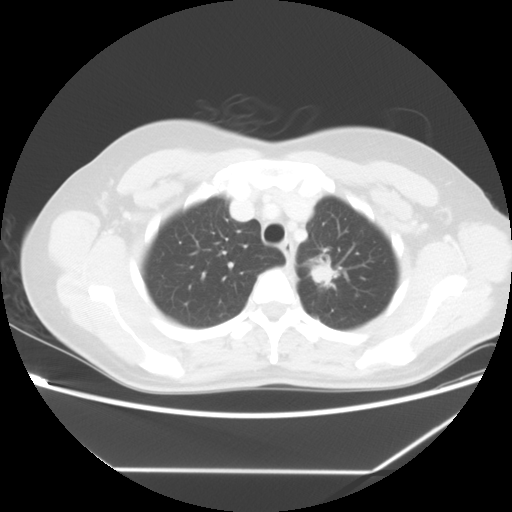
Chest CT, one axial slice. Slice 48 of 60 in the series (ordered by position). Reconstruction kernel STANDARD. 140 kVp. Lung window (W 1500 / L -600 HU). 512 × 512 image matrix, field of view 367 × 367 mm. Female patient, age 43 years. Case-level facts recorded for this patient, not image findings: clinical TNM (as recorded): T1c N0 M1b.
Annotated regions visible in this slice (bounding box drawn by a radiologist):
- lung tumour (recorded histology: adenocarcinoma): box from (x=308, y=256) to (x=337, y=294) px